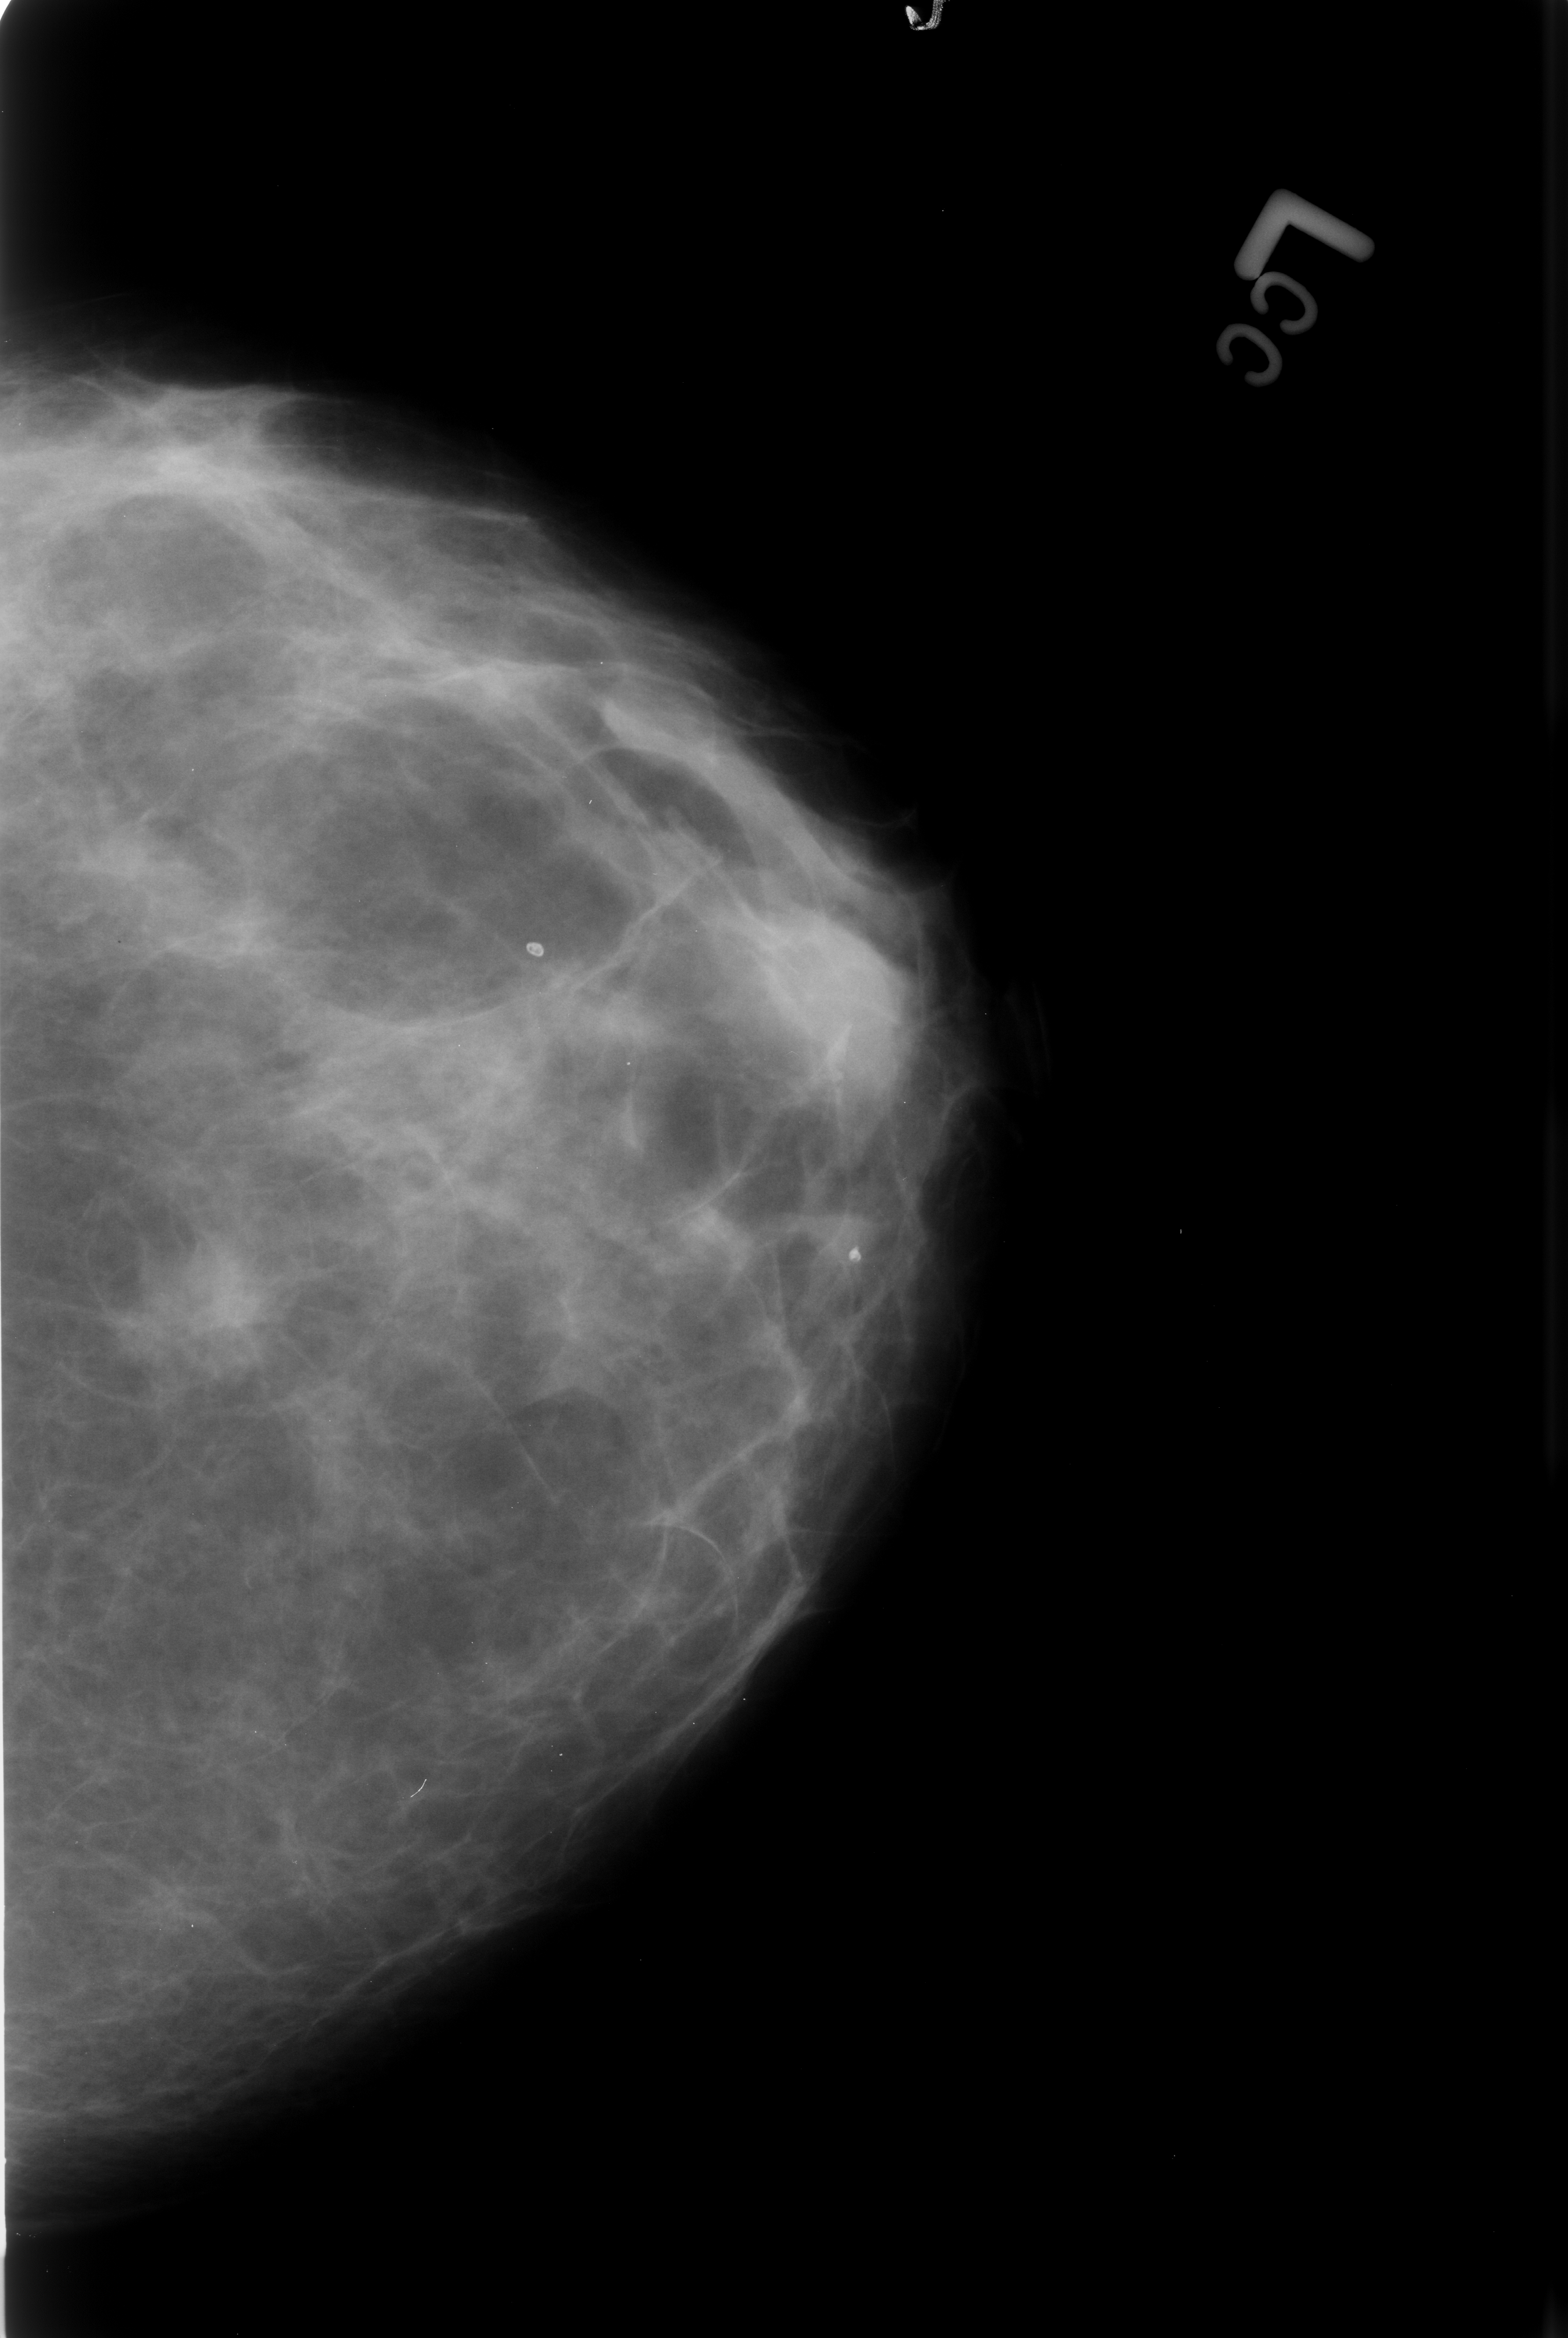
Digitized screen-film mammogram, left breast, craniocaudal (CC) view, breast composition: scattered fibroglandular densities (BI-RADS density category 2 of 4).
- Marked abnormality: mass, shape irregular, margins ill defined / spiculated; BI-RADS assessment category 4; pathology (as recorded): malignant.